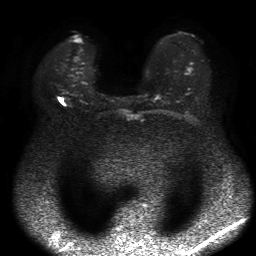
Breast MRI, one axial slice; position 33 of 50 along the scan axis; diffusion-weighted series; image 2 of 4 stored at this slice position (different b-values; order by instance number); 1.5 T; 4 mm slice thickness; 256 × 256 image matrix, field of view 360 × 360 mm. Female patient.
Annotated regions visible in this slice (outlined manually by an expert reader):
- tumour on diffusion-weighted imaging: bounding box [x1, y1, x2, y2] px = [59, 98, 63, 102]